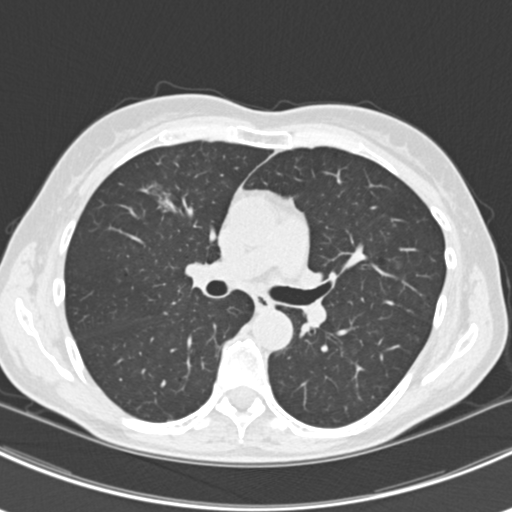
Axial slice from a low-dose chest CT screening exam. Baseline annual screen. Lung window (W 1500 / L -600 HU). Standard (soft-tissue) reconstruction kernel (B30f). Female participant, aged 63 years at enrolment.
• Lesion marked by an expert reader, bounding box [x1, y1, x2, y2] px = [145, 177, 201, 232].
• The screening reader recorded 10 non-calcified nodules or masses ≥4 mm on this exam (right lower lobe, right lower lobe, left lower lobe, left lower lobe, right middle lobe, right lower lobe, left lower lobe, left upper lobe, right upper lobe, left upper lobe); which of them this box marks is not recorded.
• Lung cancer was diagnosed 751 days after this screen: bronchiolo-alveolar adenocarcinoma, NOS, right upper lobe, right middle lobe, right lower lobe, left upper lobe, left lower lobe, moderately differentiated (G2), stage IV (AJCC 6th edition).